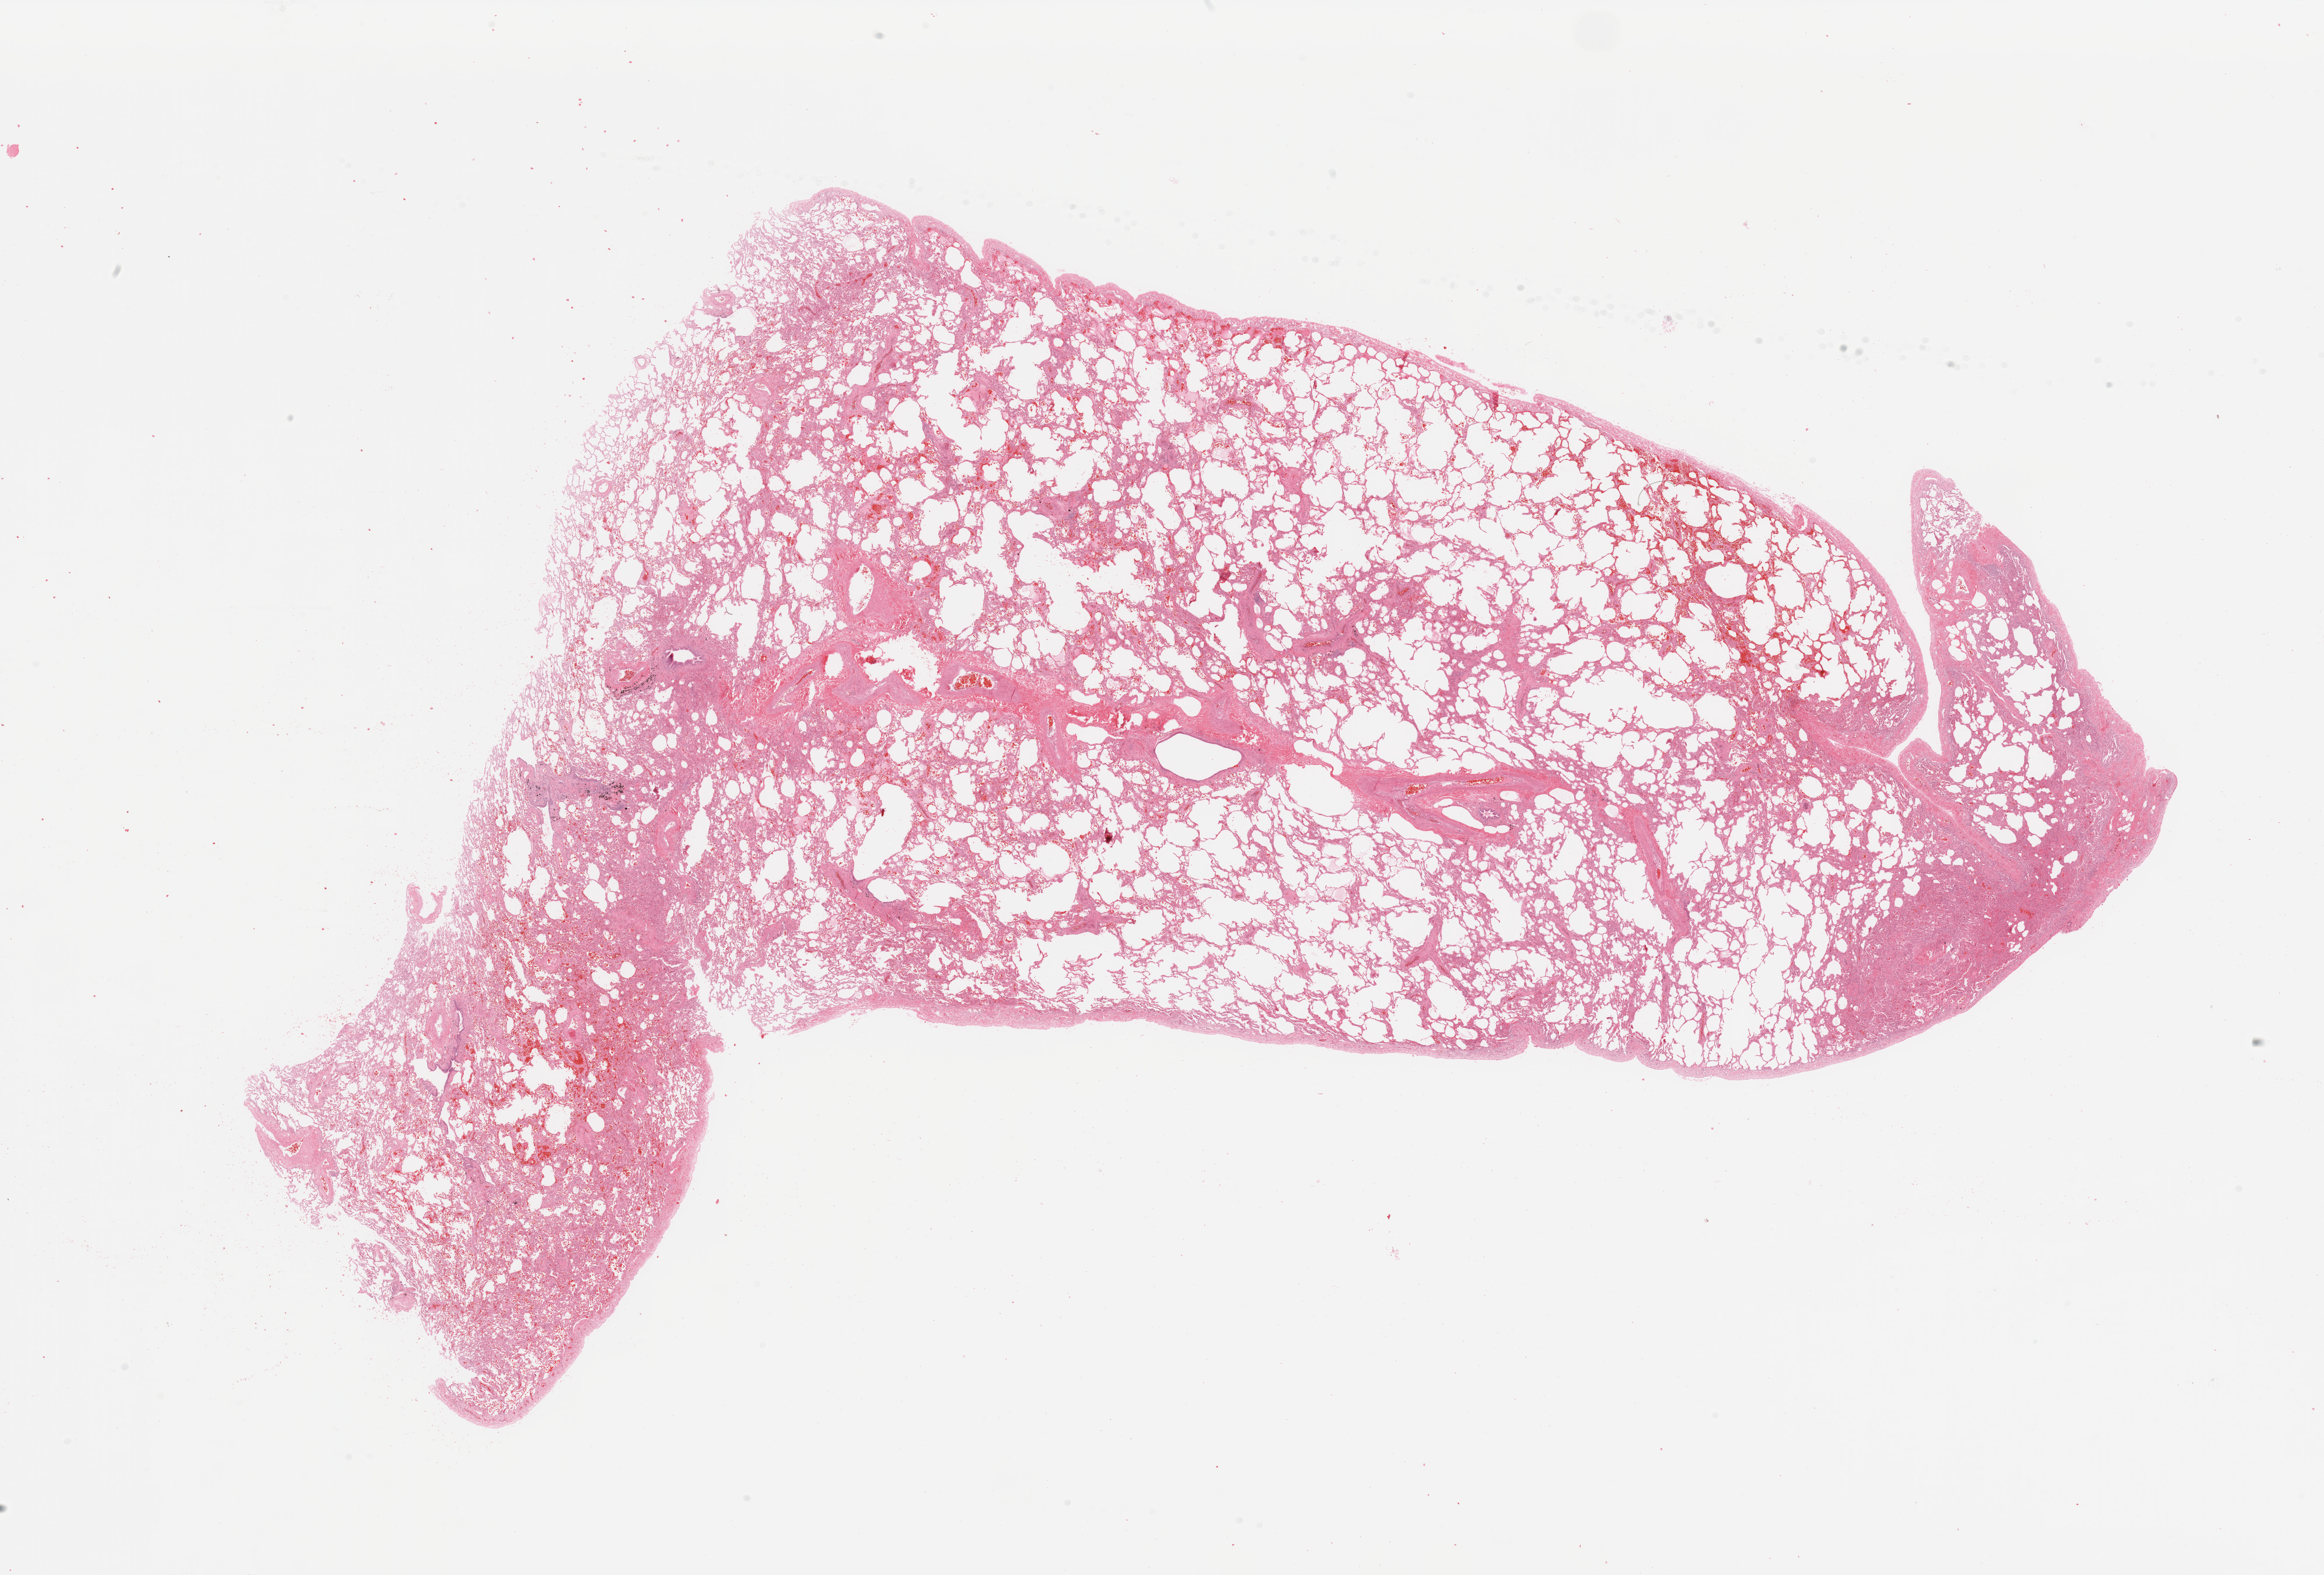
Digitized Hematoxylin and eosin (H&E) stained tissue section (whole slide) — a low-resolution overview of the entire scanned area, about 31.5 x 21.3 mm, normal (non-tumour) tissue sample, sampled site: lung. Female, 48 y/o.
This section: normal (non-tumour) tissue from the same patient. Patient diagnosis: Adenocarcinoma, NOS.